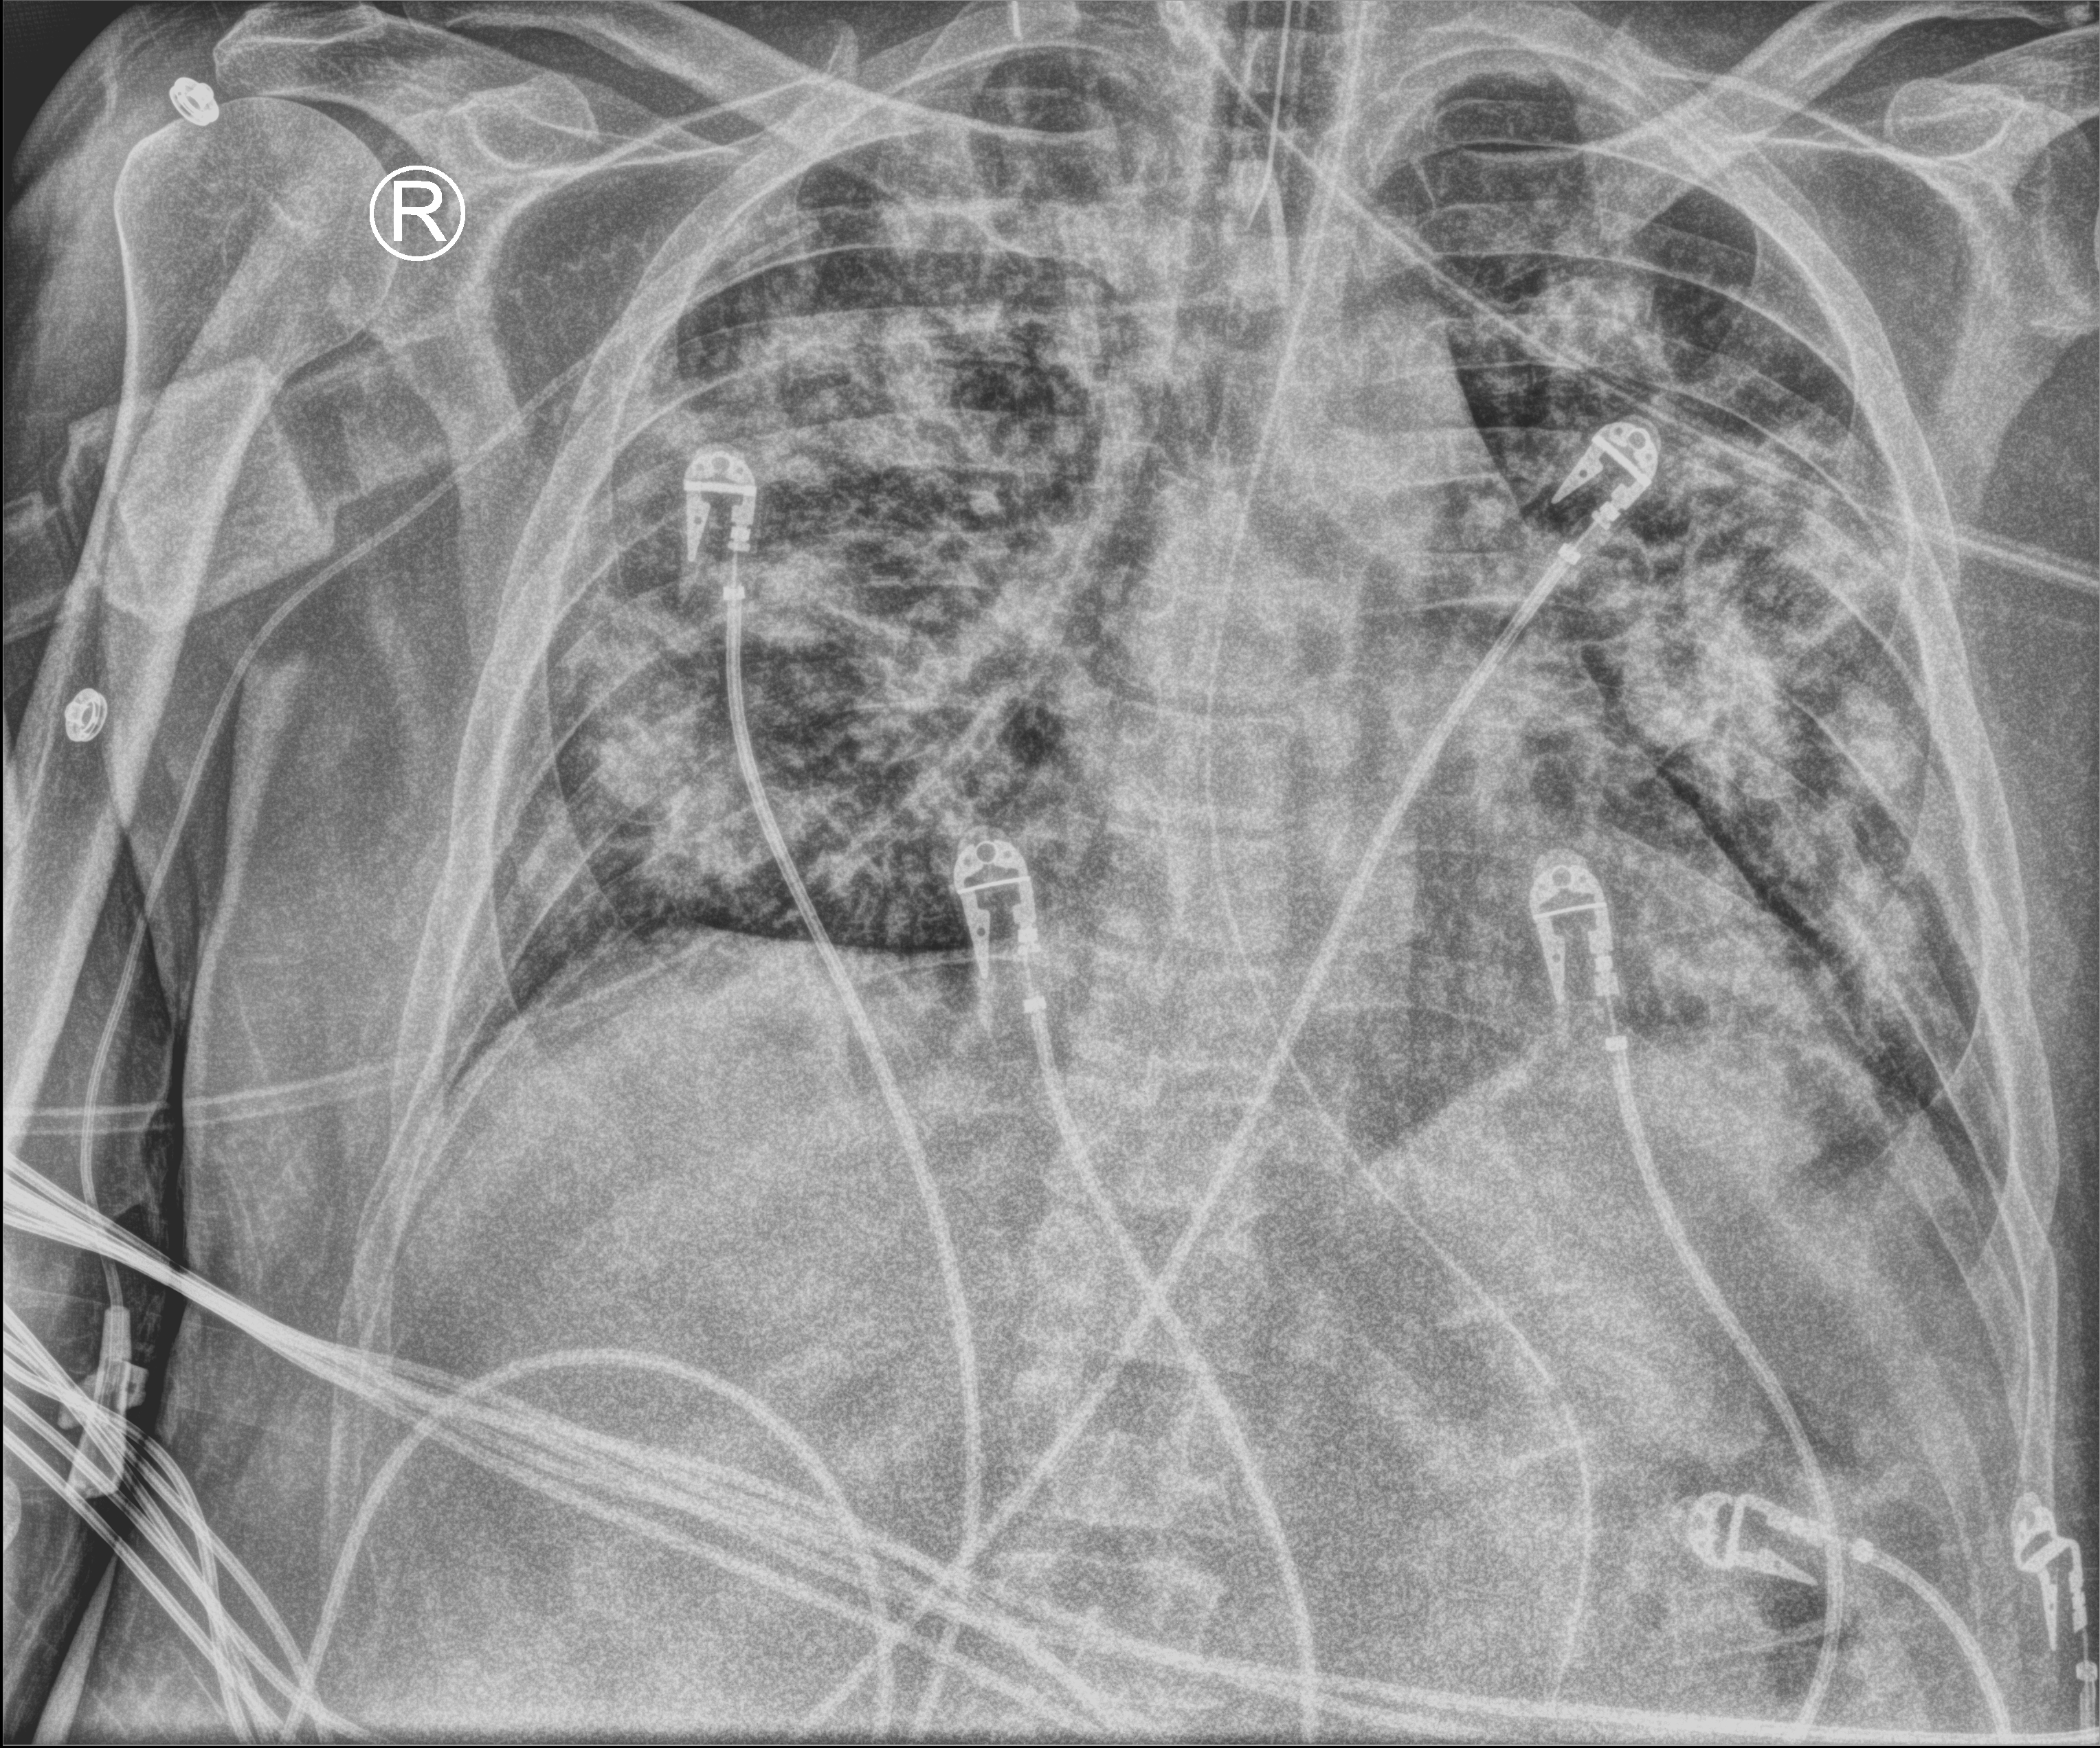
Chest X-ray (portable), anteroposterior (AP) projection. Patient hospitalised with COVID-19; male, aged 18–59 years.
From the hospital-stay record, not from the radiograph (when in the stay this image was taken is not recorded):
- admitted to intensive care during this hospital stay: yes
- mechanically ventilated during this hospital stay: yes